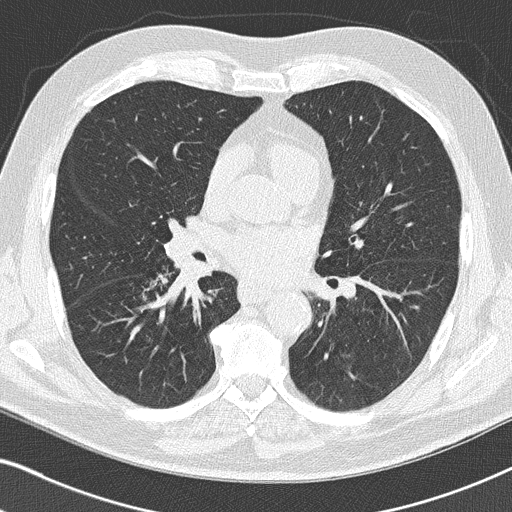
Chest CT (low-dose screening protocol), one axial image. Third screening round (two years after baseline). Lung window (W 1500 / L -600 HU). 2 mm slice thickness. Slice 86 of 155 in the series. 512 × 512 image matrix, field of view 331 × 331 mm. Male, age 66 years at enrolment. Current smoker at enrolment.
• Lesion marked by an expert reader, bounding box [x1, y1, x2, y2] px = [136, 268, 228, 331].
• Reader record for this screening exam (exam-level; its link to the box is not recorded): non-calcified nodule or mass ≥4 mm, right upper lobe, 5 × 4 mm, smooth margins, pre-existing on the prior screen: yes; interval growth: no.
• Official screen result: positive, other.